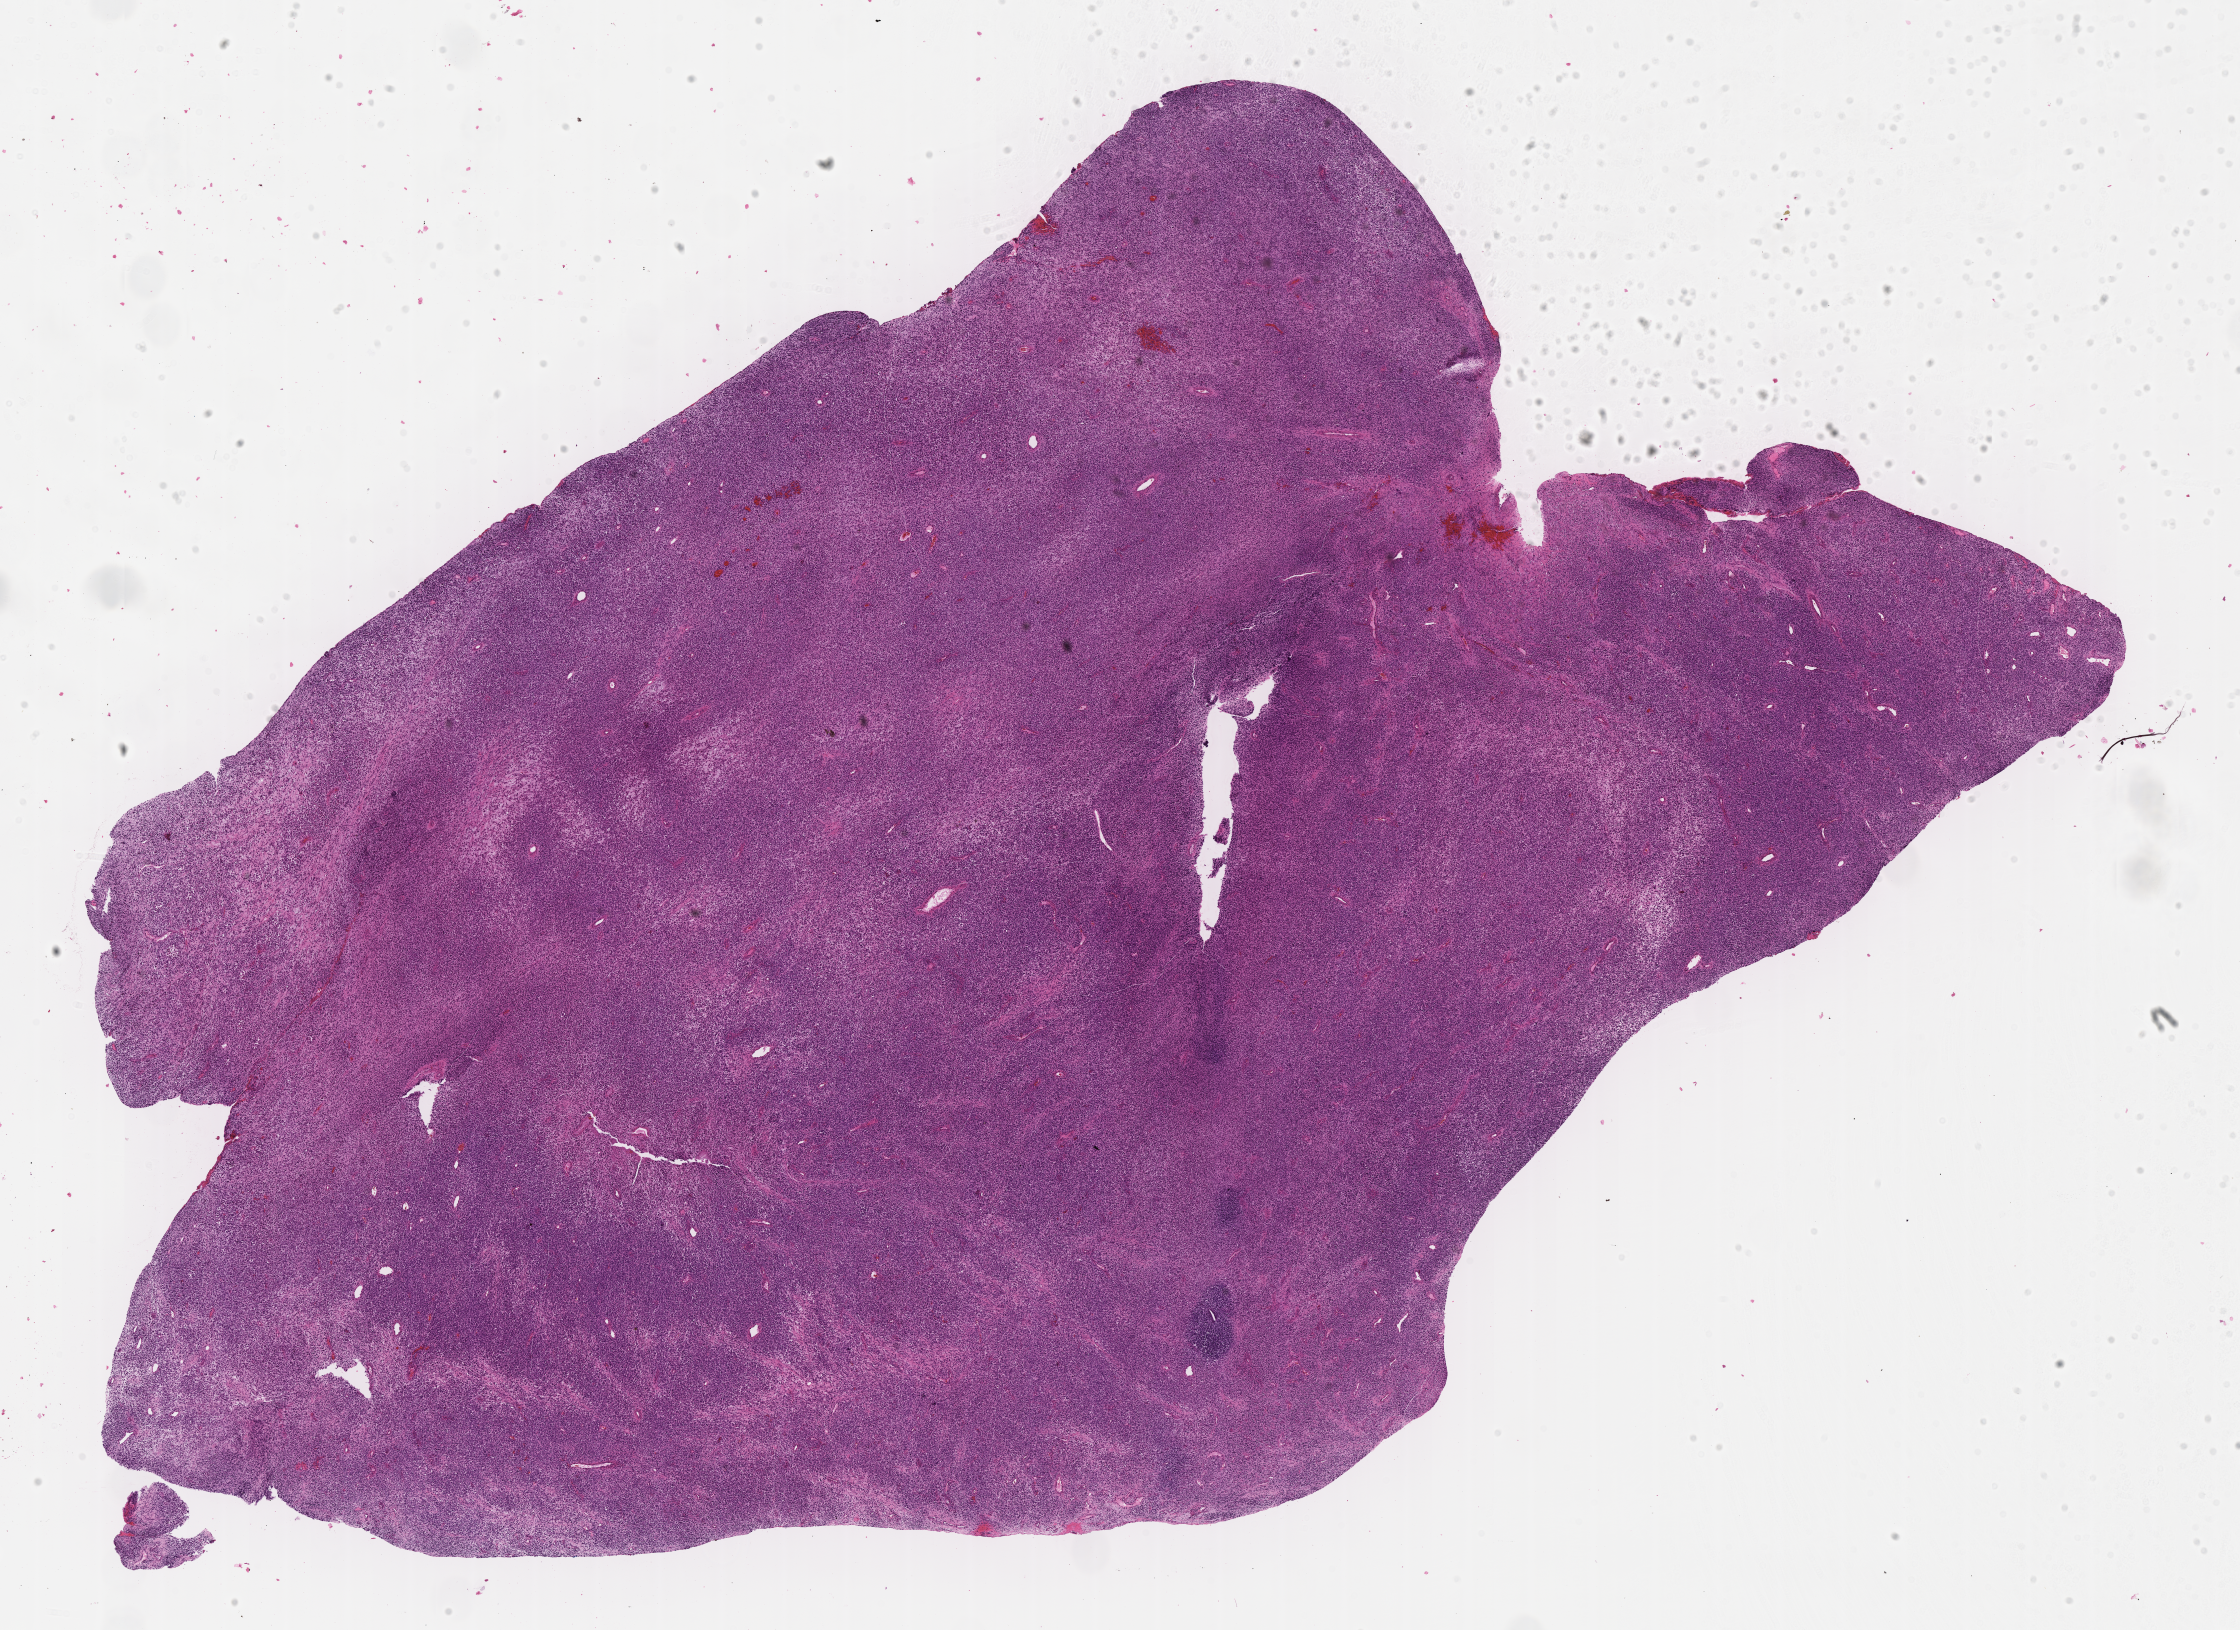
H&E whole-slide image of tumor tissue, low-resolution overview of the scanned area, about 18.1 x 13.2 mm. Formalin-fixed paraffin-embedded section. Site: abdomen. Male patient, age at diagnosis 2.2 years.
Metastatic status at presentation (as recorded): non-metastatic. Diagnosis: rhabdomyosarcoma; histological classification: embryonal rhabdomyosarcoma. Stage (as recorded): 3. Primary site (case record): perineum.